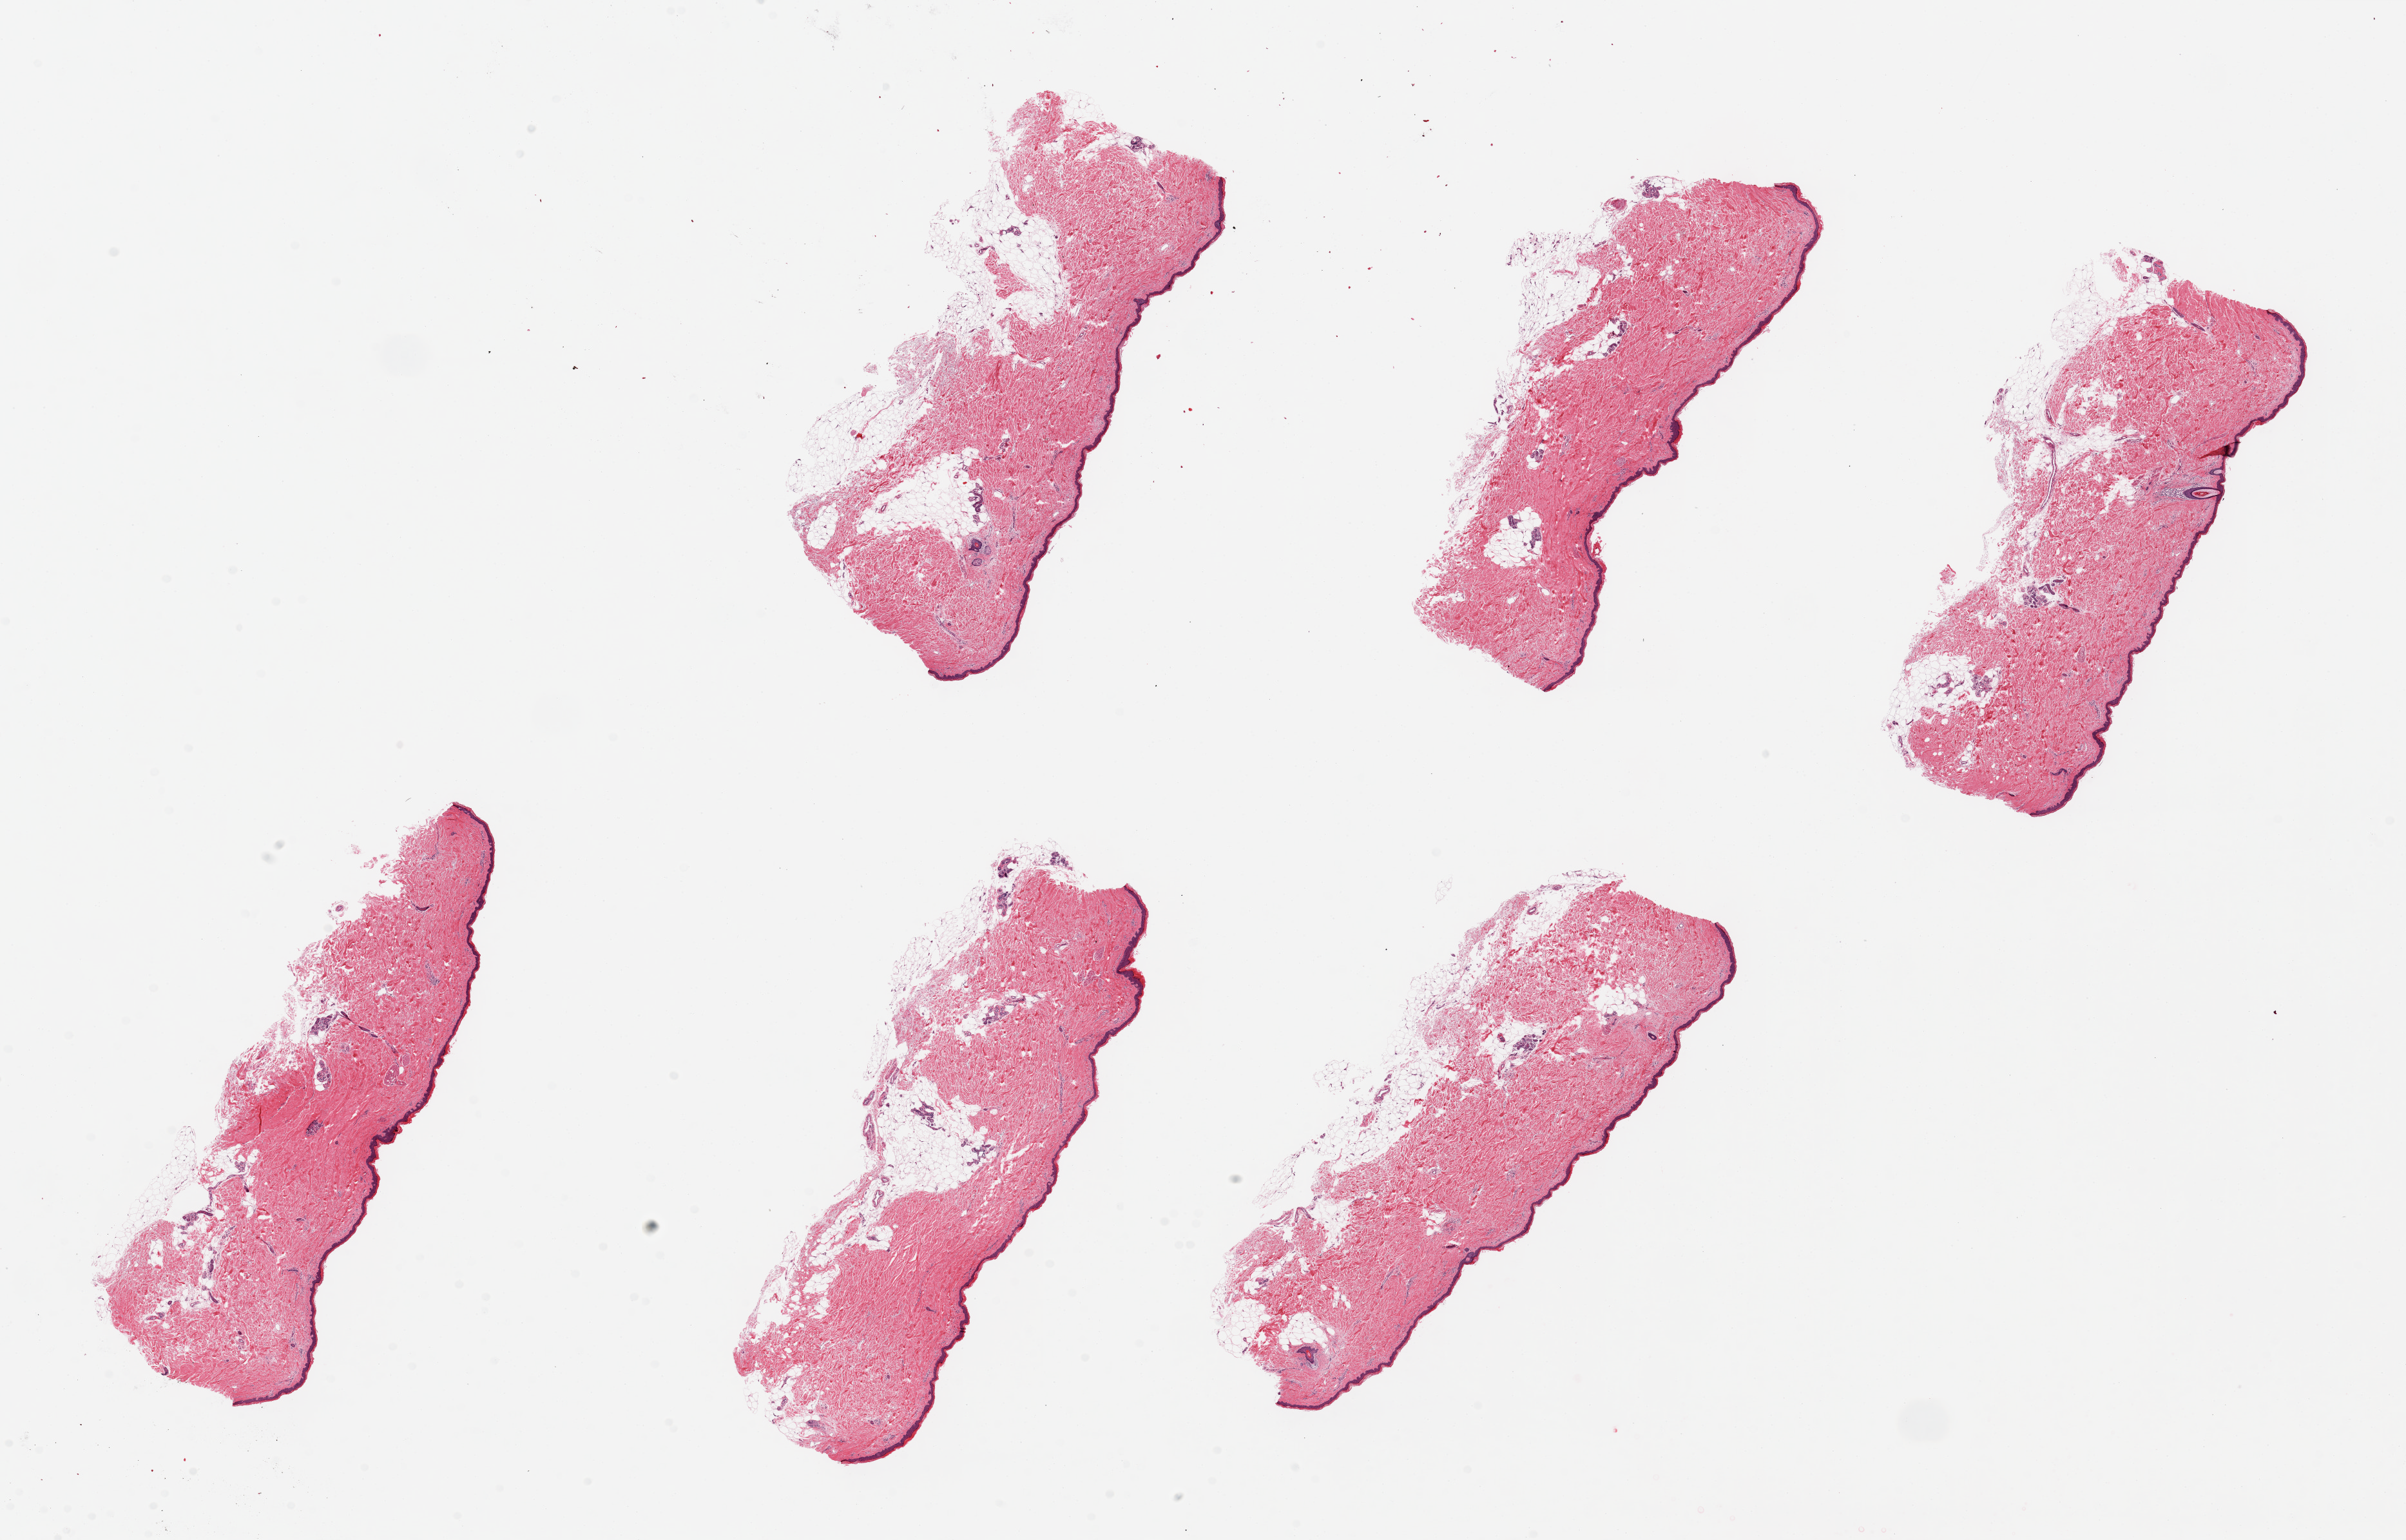
Digitized H&E-stained section, whole scanned area (about 29.5 x 18.9 mm, acquisition: 20x scan) shown as a low-resolution overview, PAXgene-fixed paraffin-embedded (PFPE) section, section of skin of lower leg (target tissue), donor tissue sample. Female donor.
- pathologist's review note for this sample: 6pieces ~7x3mm; squamous epithelium is ~1-2% thickness